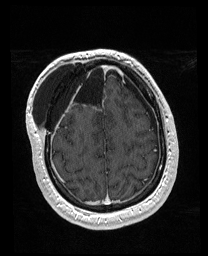
Brain MRI from a brain-tumour surgery series, one axial slice; slice 50 of 176 in the series (ordered by position); T1-weighted post-contrast; 1 mm slice thickness; 208 × 256 image matrix, field of view 208 × 256 mm. Case-level facts recorded for this patient, not image findings: histopathology: Astrocytoma; WHO grade: 4; IDH mutation: yes; tumour location: Right Orbitofrontal Anterior Temporal Insular.
Structures marked on this image (expert manual segmentation):
- previous resection cavity: bounding box [x1, y1, x2, y2] px = [56, 63, 106, 105]